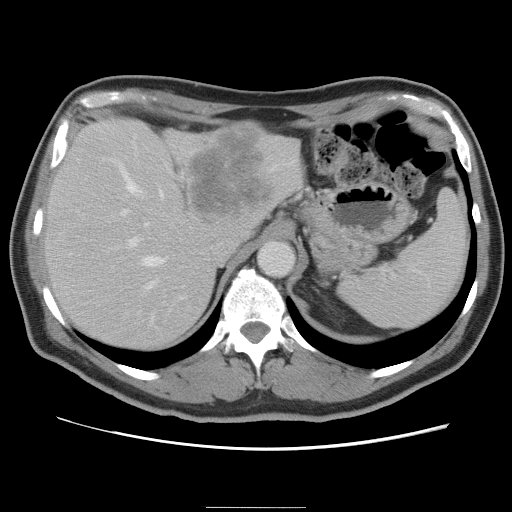
Contrast-enhanced abdominal CT, one axial slice; position 58 of 87 along the scan axis; 120 kVp; intravenous contrast given; soft-tissue window (W 400 / L 40 HU); 512 × 512 image matrix, field of view 363 × 363 mm. Male patient, age 63 years. From the clinical record (not read from this slice): diagnosis: colorectal cancer liver metastases, imaged before liver resection; multiple liver metastases: no; largest metastasis: 9 cm.
Annotated regions visible in this slice (outlined manually by an expert reader):
- hepatic veins: bounding box (x1, y1, x2, y2) in pixels: (109, 159, 167, 322)
- liver: (43, 118, 305, 351)
- planned liver remnant (the part of the liver to remain after resection): (43, 154, 217, 351)
- portal vein (with intrahepatic branches): (117, 209, 185, 300)
- liver metastasis: (190, 126, 271, 215)